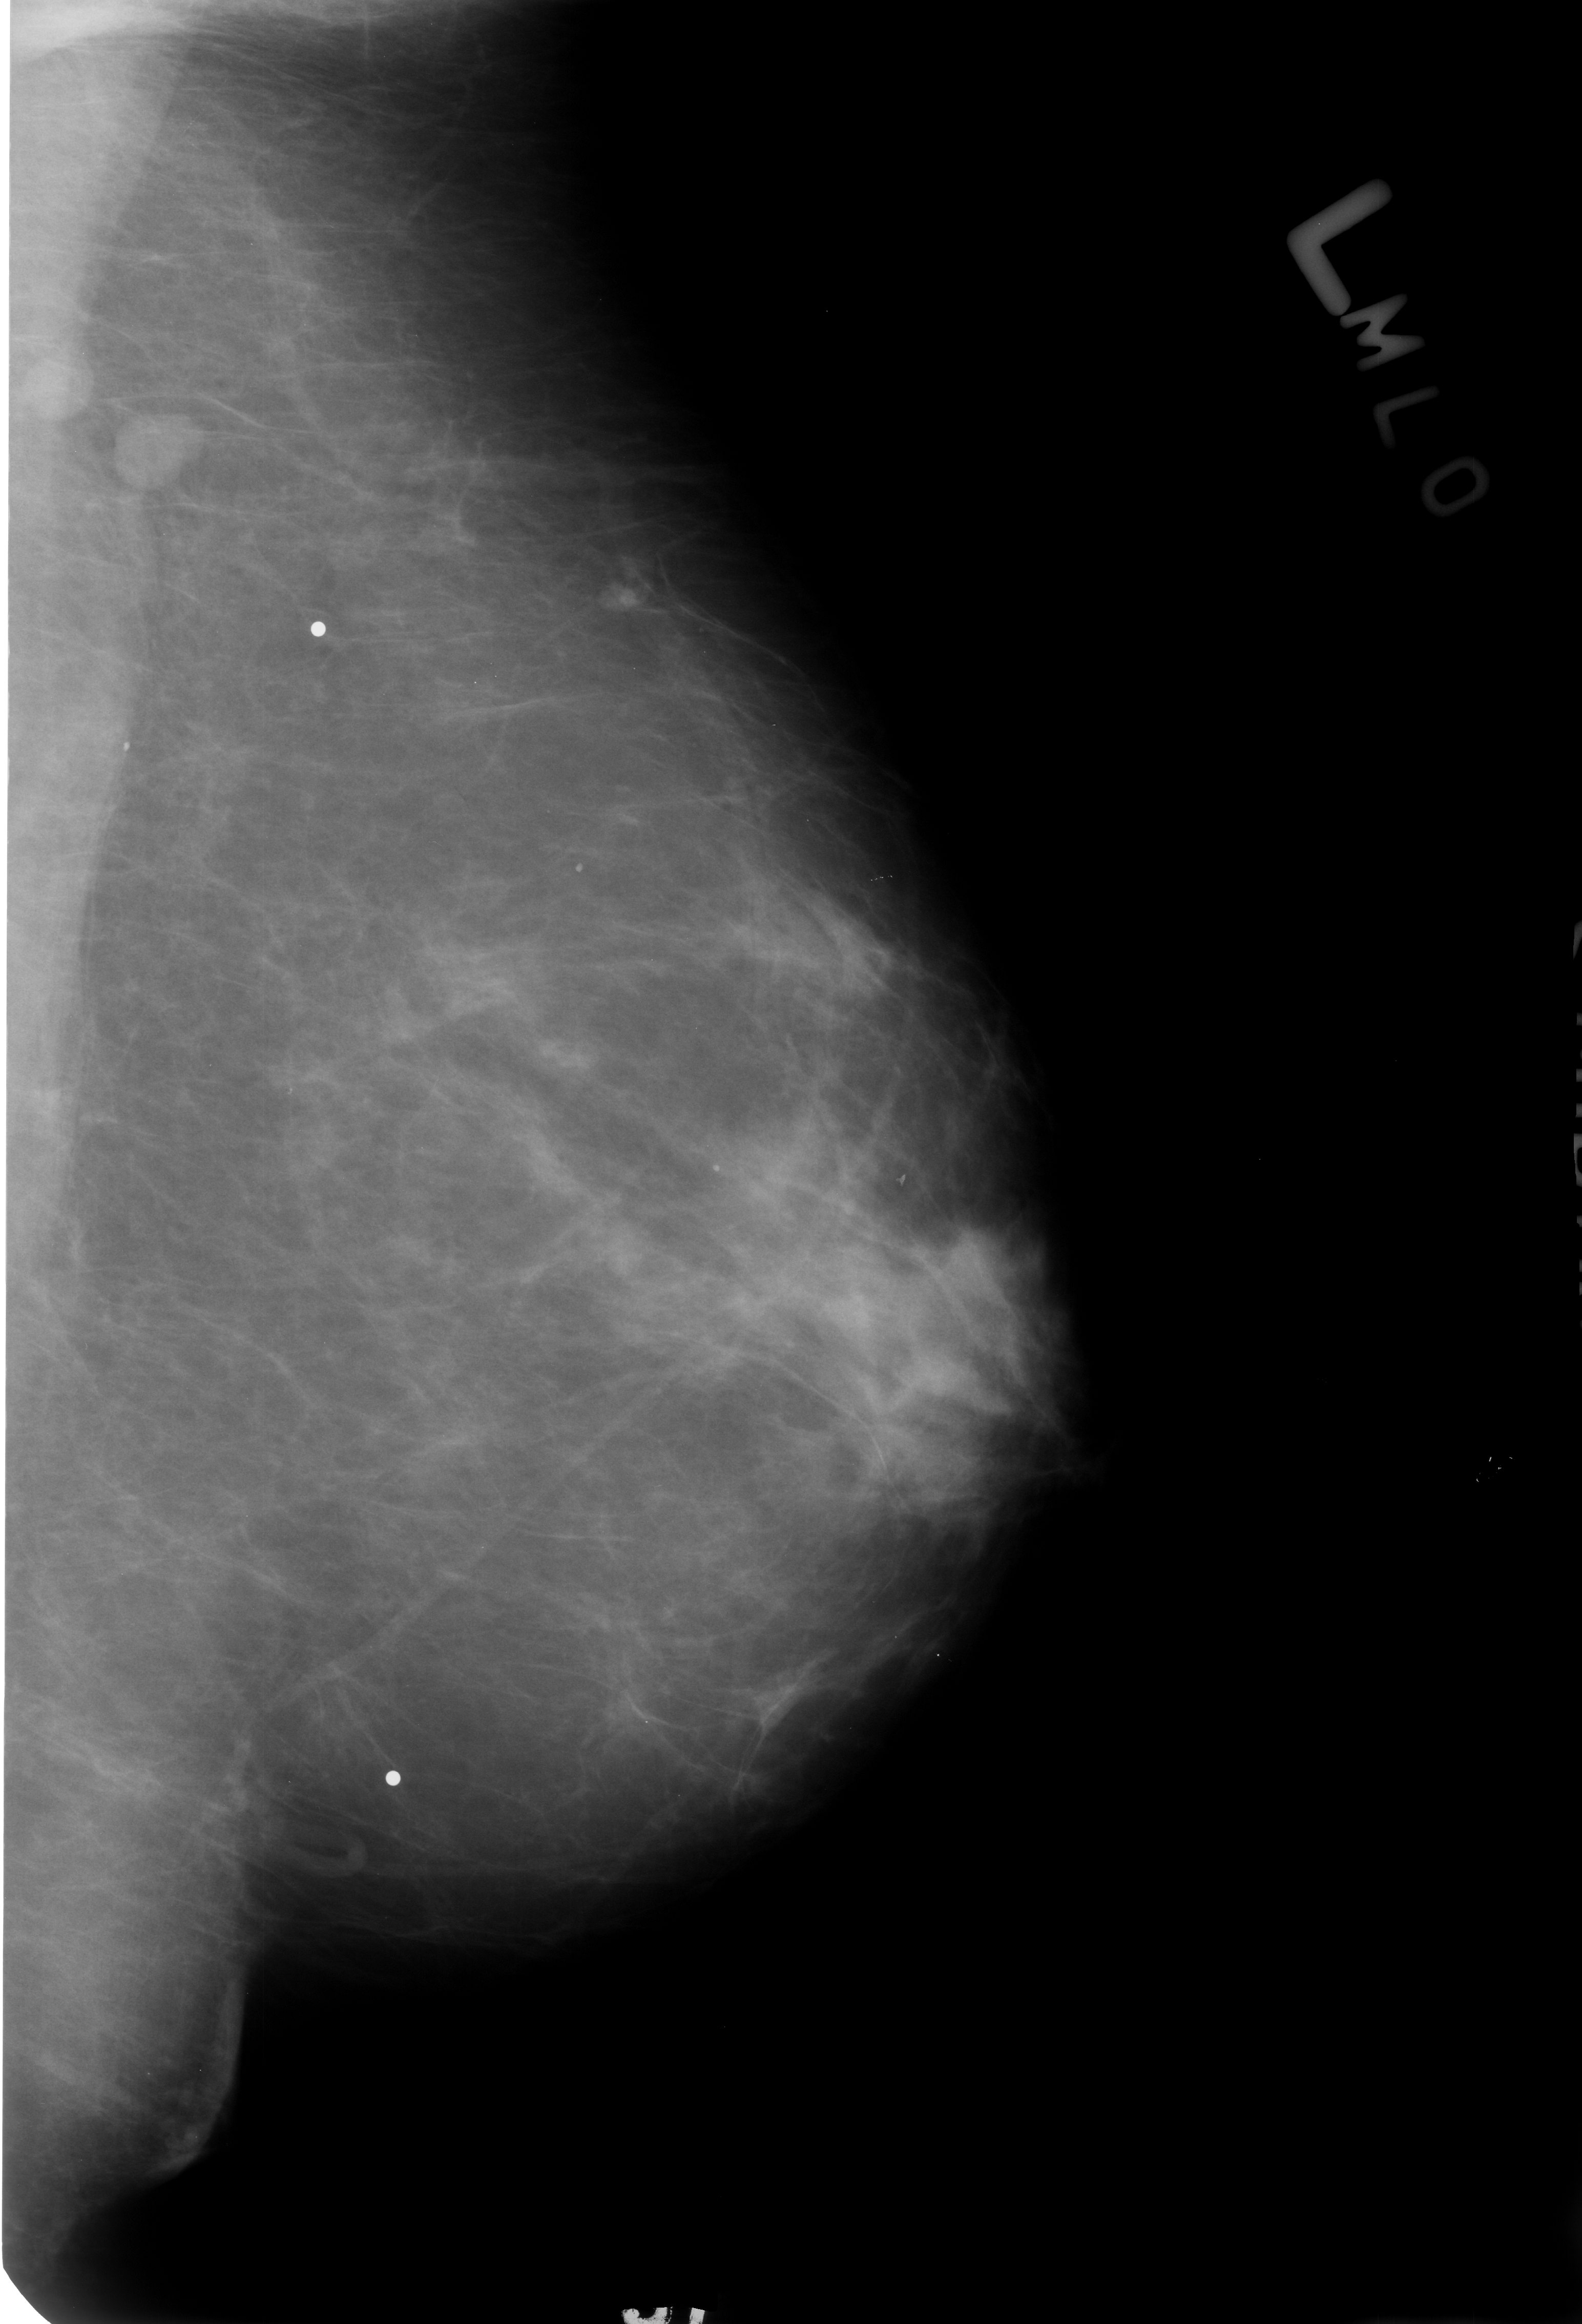
Scanned film-screen mammogram; left breast; MLO view; BI-RADS breast density category 2 (scale 1–4); 1582 × 2324 image matrix.
Expert-marked regions of interest on this image (one box per marked abnormality):
- Finding 1 of 3: calcifications, morphology punctate; BI-RADS assessment category 2; benign; no additional work-up was recommended (outcome (as recorded, no biopsy): benign without callback): bounding box [x1, y1, x2, y2] px = [81, 713, 190, 800]
- Finding 2 of 3: calcifications, morphology punctate; BI-RADS assessment category 2; outcome (as recorded, no biopsy): benign without callback (not worked up further): [540, 827, 649, 907]
- Finding 3 of 3: calcifications, morphology punctate; BI-RADS assessment category 2; subtlety rating 3 on a 1 (subtle) to 5 (obvious) scale; benign; no additional work-up was recommended (outcome (as recorded, no biopsy): benign without callback): [668, 1127, 776, 1218]